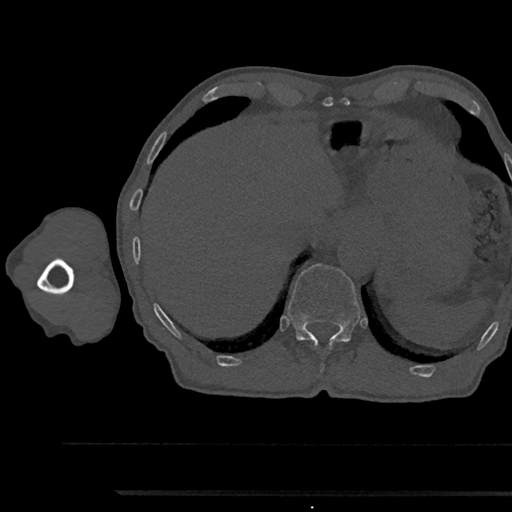
CT including the spine, one axial slice; slice 742 of 797 in the series (ordered by position); 120 kVp; bone window (W 1800 / L 400 HU); 512 × 512 image matrix, field of view 367 × 367 mm. Patient: male, 79 years. Case-level facts recorded for this patient, not image findings: primary cancer: prostate.
Structures marked on this image (semi-automatically segmented with operator editing):
- T12 vertebra: bounding box [x1, y1, x2, y2] px = [288, 264, 360, 346]